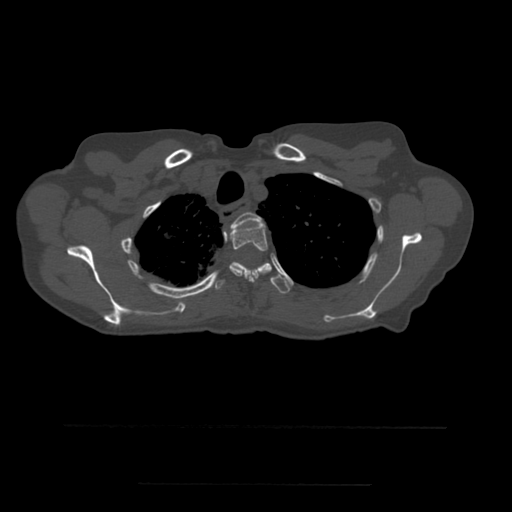
CT including the spine, one axial slice; slice 418 of 544 in the series (ordered by position); bone window (W 1800 / L 400 HU); 1.25 mm slice thickness; 512 × 512 image matrix, field of view 350 × 350 mm. Patient age 58 years. Case-level facts recorded for this patient, not image findings: primary cancer: lung.
Annotated regions visible in this slice (semi-automatic segmentation, software-assisted and operator-edited):
- T2 vertebra: bounding box <224,212,262,237> (left, top, right, bottom; pixels)
- T3 vertebra: <230,221,272,282>
- T4 vertebra: <212,262,291,294>